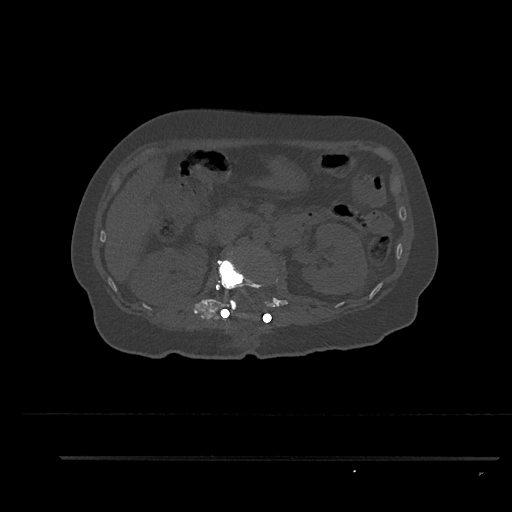
CT including the spine, one axial slice. Reconstruction kernel Br40s/3. Bone window (W 1800 / L 400 HU). 0.5 mm slice thickness. 512 × 512 image matrix, field of view 408 × 408 mm. Patient: female, 44 years. From the clinical record (not read from this slice): primary cancer: renal; vertebrae with lytic lesions (as recorded): L1.
Structures marked on this image (semi-automatic segmentation, software-assisted and operator-edited):
- L1 vertebra: box from (x=218, y=257) to (x=278, y=317) px
- L2 vertebra: (x=224, y=304)–(x=229, y=311)